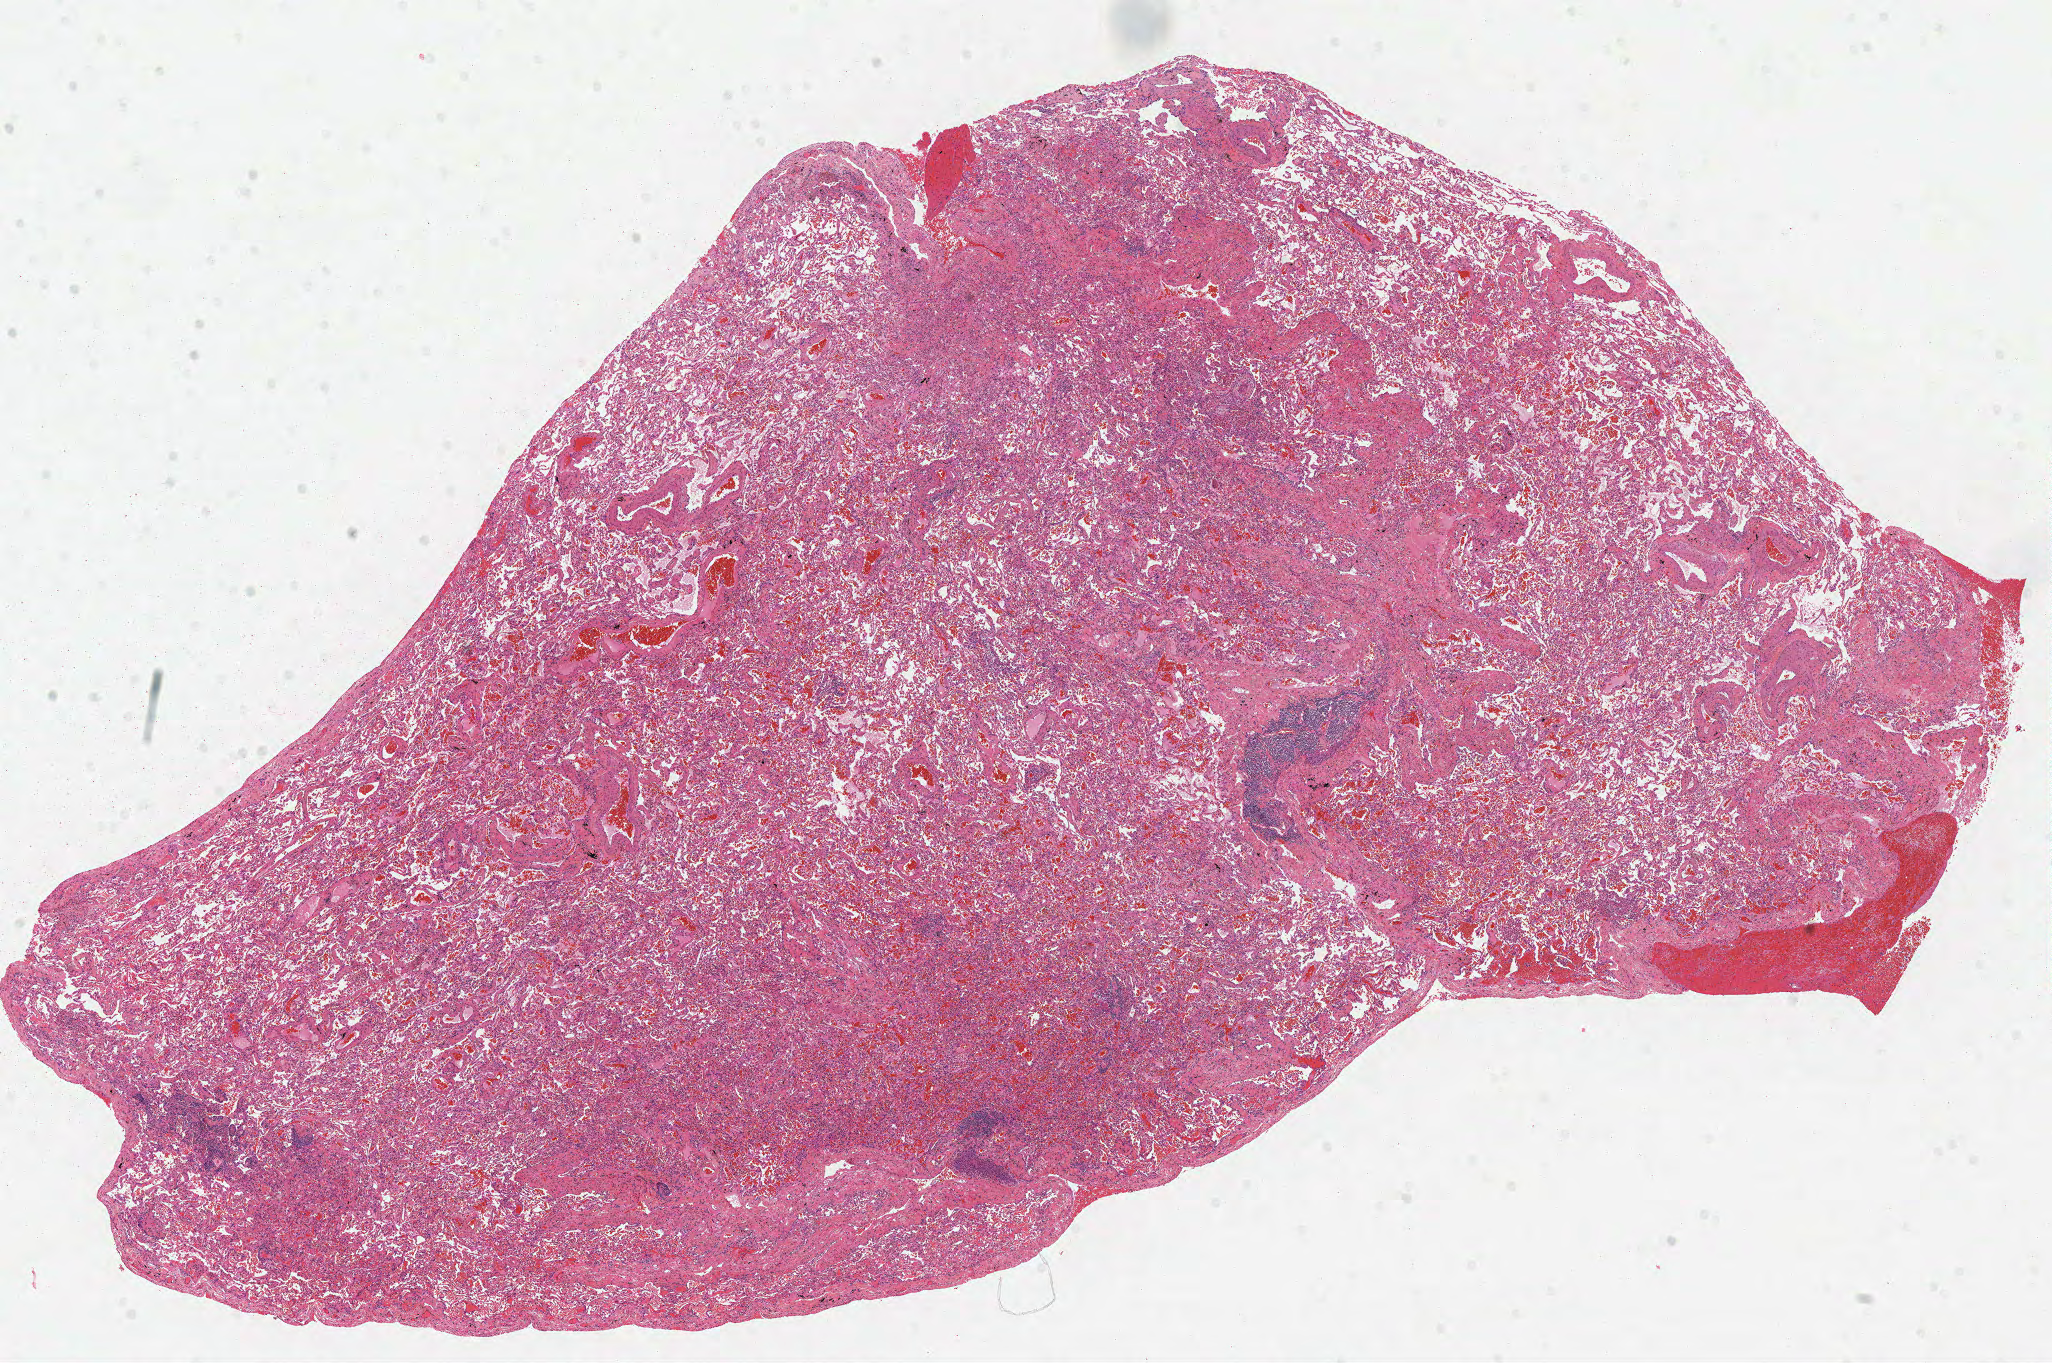
Whole-slide histology image, H&E, a low-resolution overview of the entire scanned area, about 16.2 x 10.7 mm. Frozen section from the top of the tissue portion. Solid tissue normal (non-tumour tissue) sample from the lung. Male, age 66 years at initial diagnosis.
This section: solid tissue normal sample (biorepository sample class). Patient diagnosis: Adenocarcinoma, NOS.